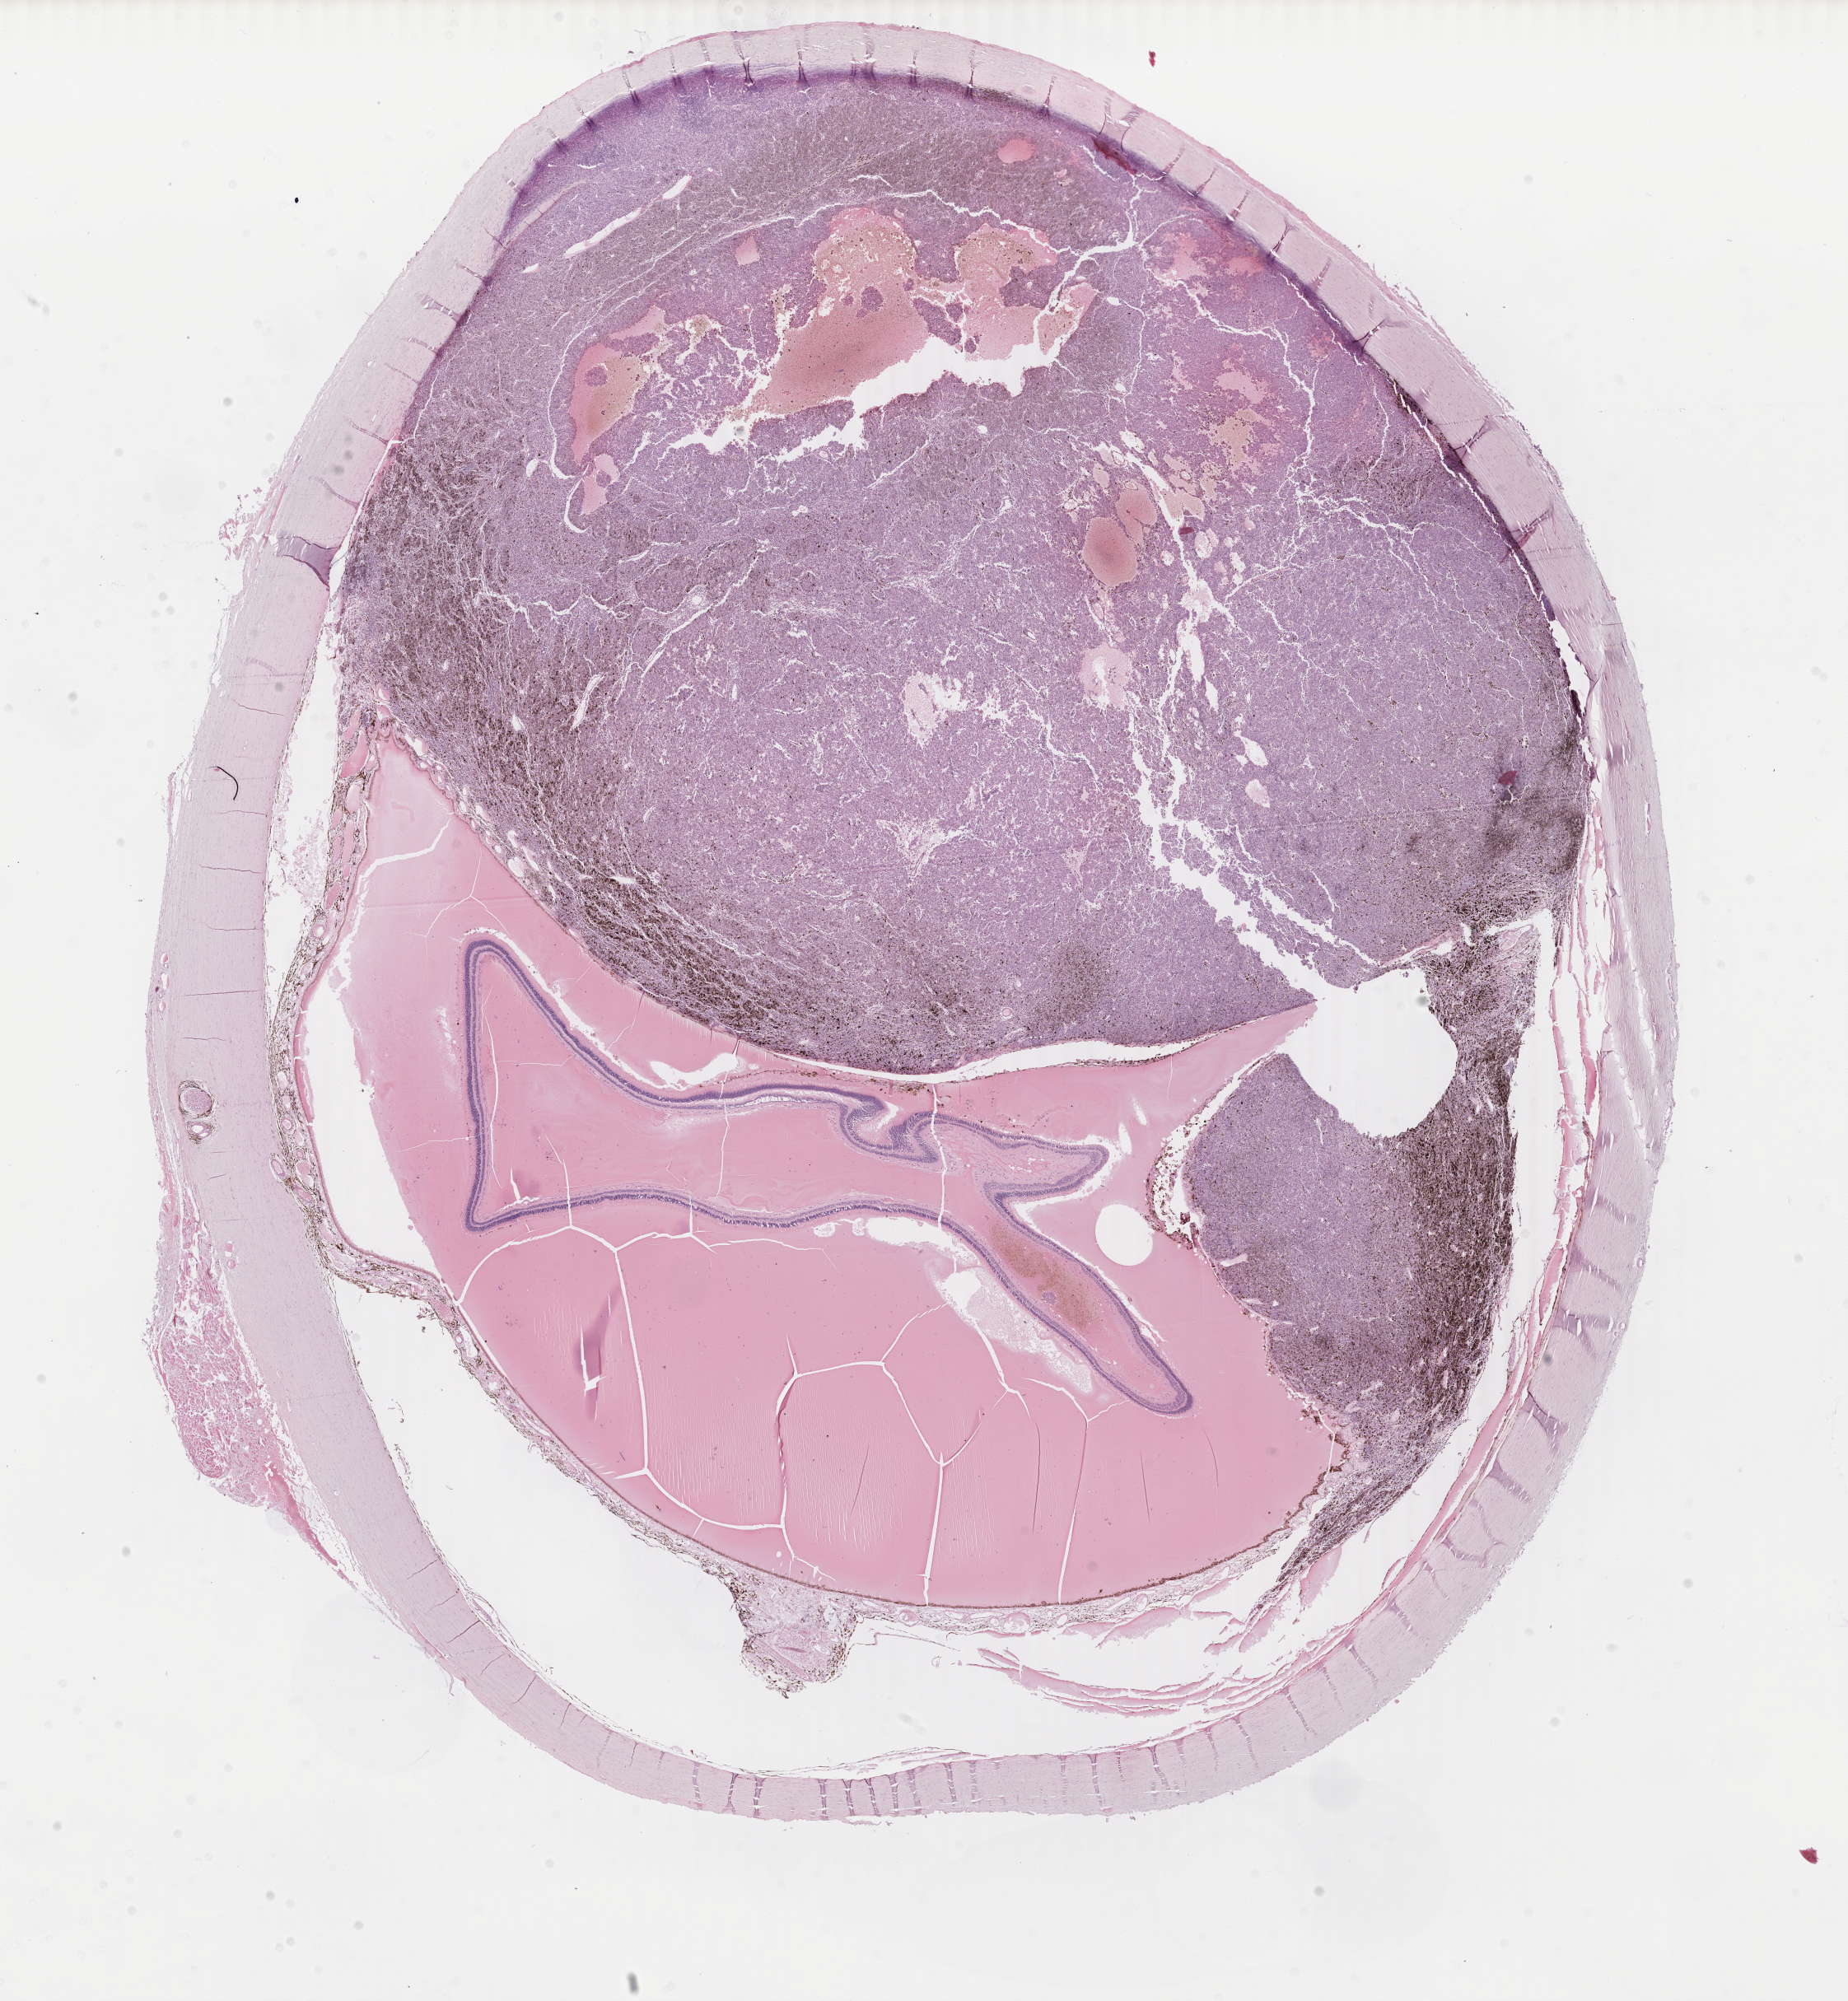
Digitized H&E-stained tissue section (whole slide) — whole scanned area (about 17.8 x 19.3 mm) shown as a low-resolution overview; formalin-fixed paraffin-embedded (FFPE) diagnostic section; primary tumour sample from the uvea. Male, age 60 years at initial diagnosis.
AJCC pathologic stage: IIIA (7th edition). Pathologic diagnosis: Epithelioid cell melanoma. TNM: T4a N0 M0.